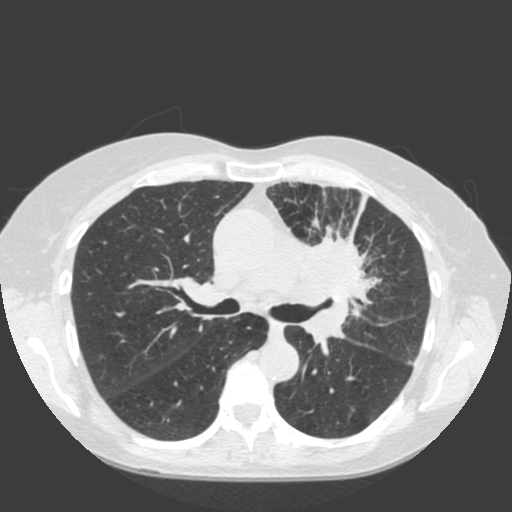
Low-dose screening chest CT, one axial slice. Position 118 of 184 along the scan axis. Lung window (W 1500 / L -600 HU). 2 mm slice thickness. 512 × 512 image matrix, field of view 350 × 350 mm.
Annotated regions visible in this slice (expert manual segmentation):
- lesion 1 (tumor, hilum of left lung): bounding box <292,231,377,356> (left, top, right, bottom; pixels)